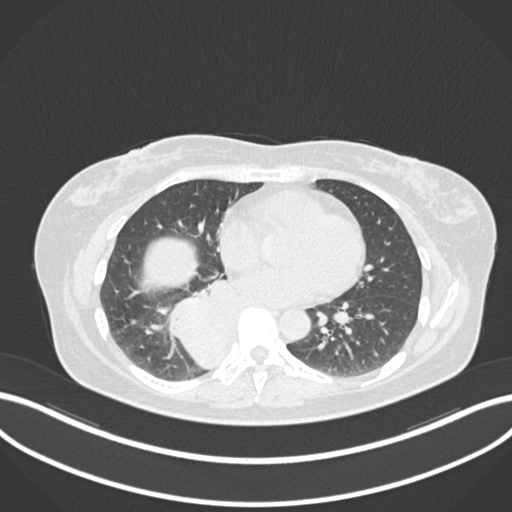
Chest CT, one axial slice. Slice 567 of 677 in the series (ordered by position). Reconstruction kernel B30f. Lung window (W 1500 / L -600 HU). 1 mm slice thickness. 512 × 512 image matrix, field of view 400 × 400 mm. Female patient, age 54 years. From the clinical record (not read from this slice): clinical TNM (as recorded): T4 N0 M0.
Structures marked on this image (bounding box drawn by a radiologist):
- lung tumour (recorded histology: adenocarcinoma): bounding box [x1, y1, x2, y2] px = [162, 264, 242, 372]